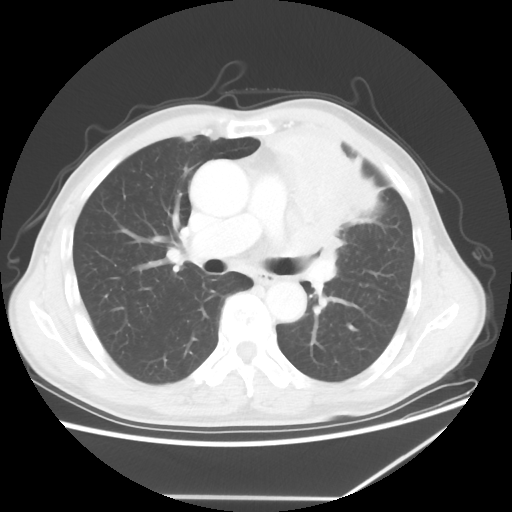
Chest CT, one axial slice; position 37 of 64 along the scan axis; reconstruction kernel STANDARD; lung window (W 1500 / L -600 HU); 5 mm slice thickness; 512 × 512 image matrix, field of view 383 × 383 mm. Male patient, age 64 years. Case-level facts recorded for this patient, not image findings: clinical TNM (as recorded): T1c N1 M1; histopathological grade: G2.
Outlined on this slice (bounding box drawn by a radiologist):
- lung tumour (recorded histology: squamous cell carcinoma): box from (x=257, y=122) to (x=427, y=292) px